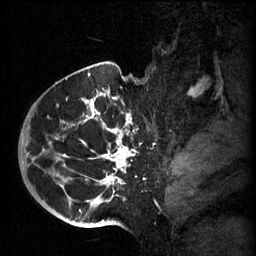
Breast MRI (dynamic contrast-enhanced), one sagittal slice; slice 45 of 60 in the series (ordered by position); 3 images stored at this slice position (order not interpretable as contrast timing); 1.5 T; TE 4.2 ms, TR 11 ms; 2 mm slice thickness; 256 × 256 image matrix, field of view 200 × 200 mm. Patient: female, 51 years.
Structures marked on this image (semi-automatic segmentation, software-assisted and operator-edited):
- analysis volume of interest (the breast-tissue region the enhancement analysis was run in; not a lesion): box from (x=48, y=82) to (x=155, y=197) px
- tumour enhancement mask (voxels above the 70 % enhancement threshold inside the analysis volume of interest): (x=62, y=92)–(x=136, y=197)